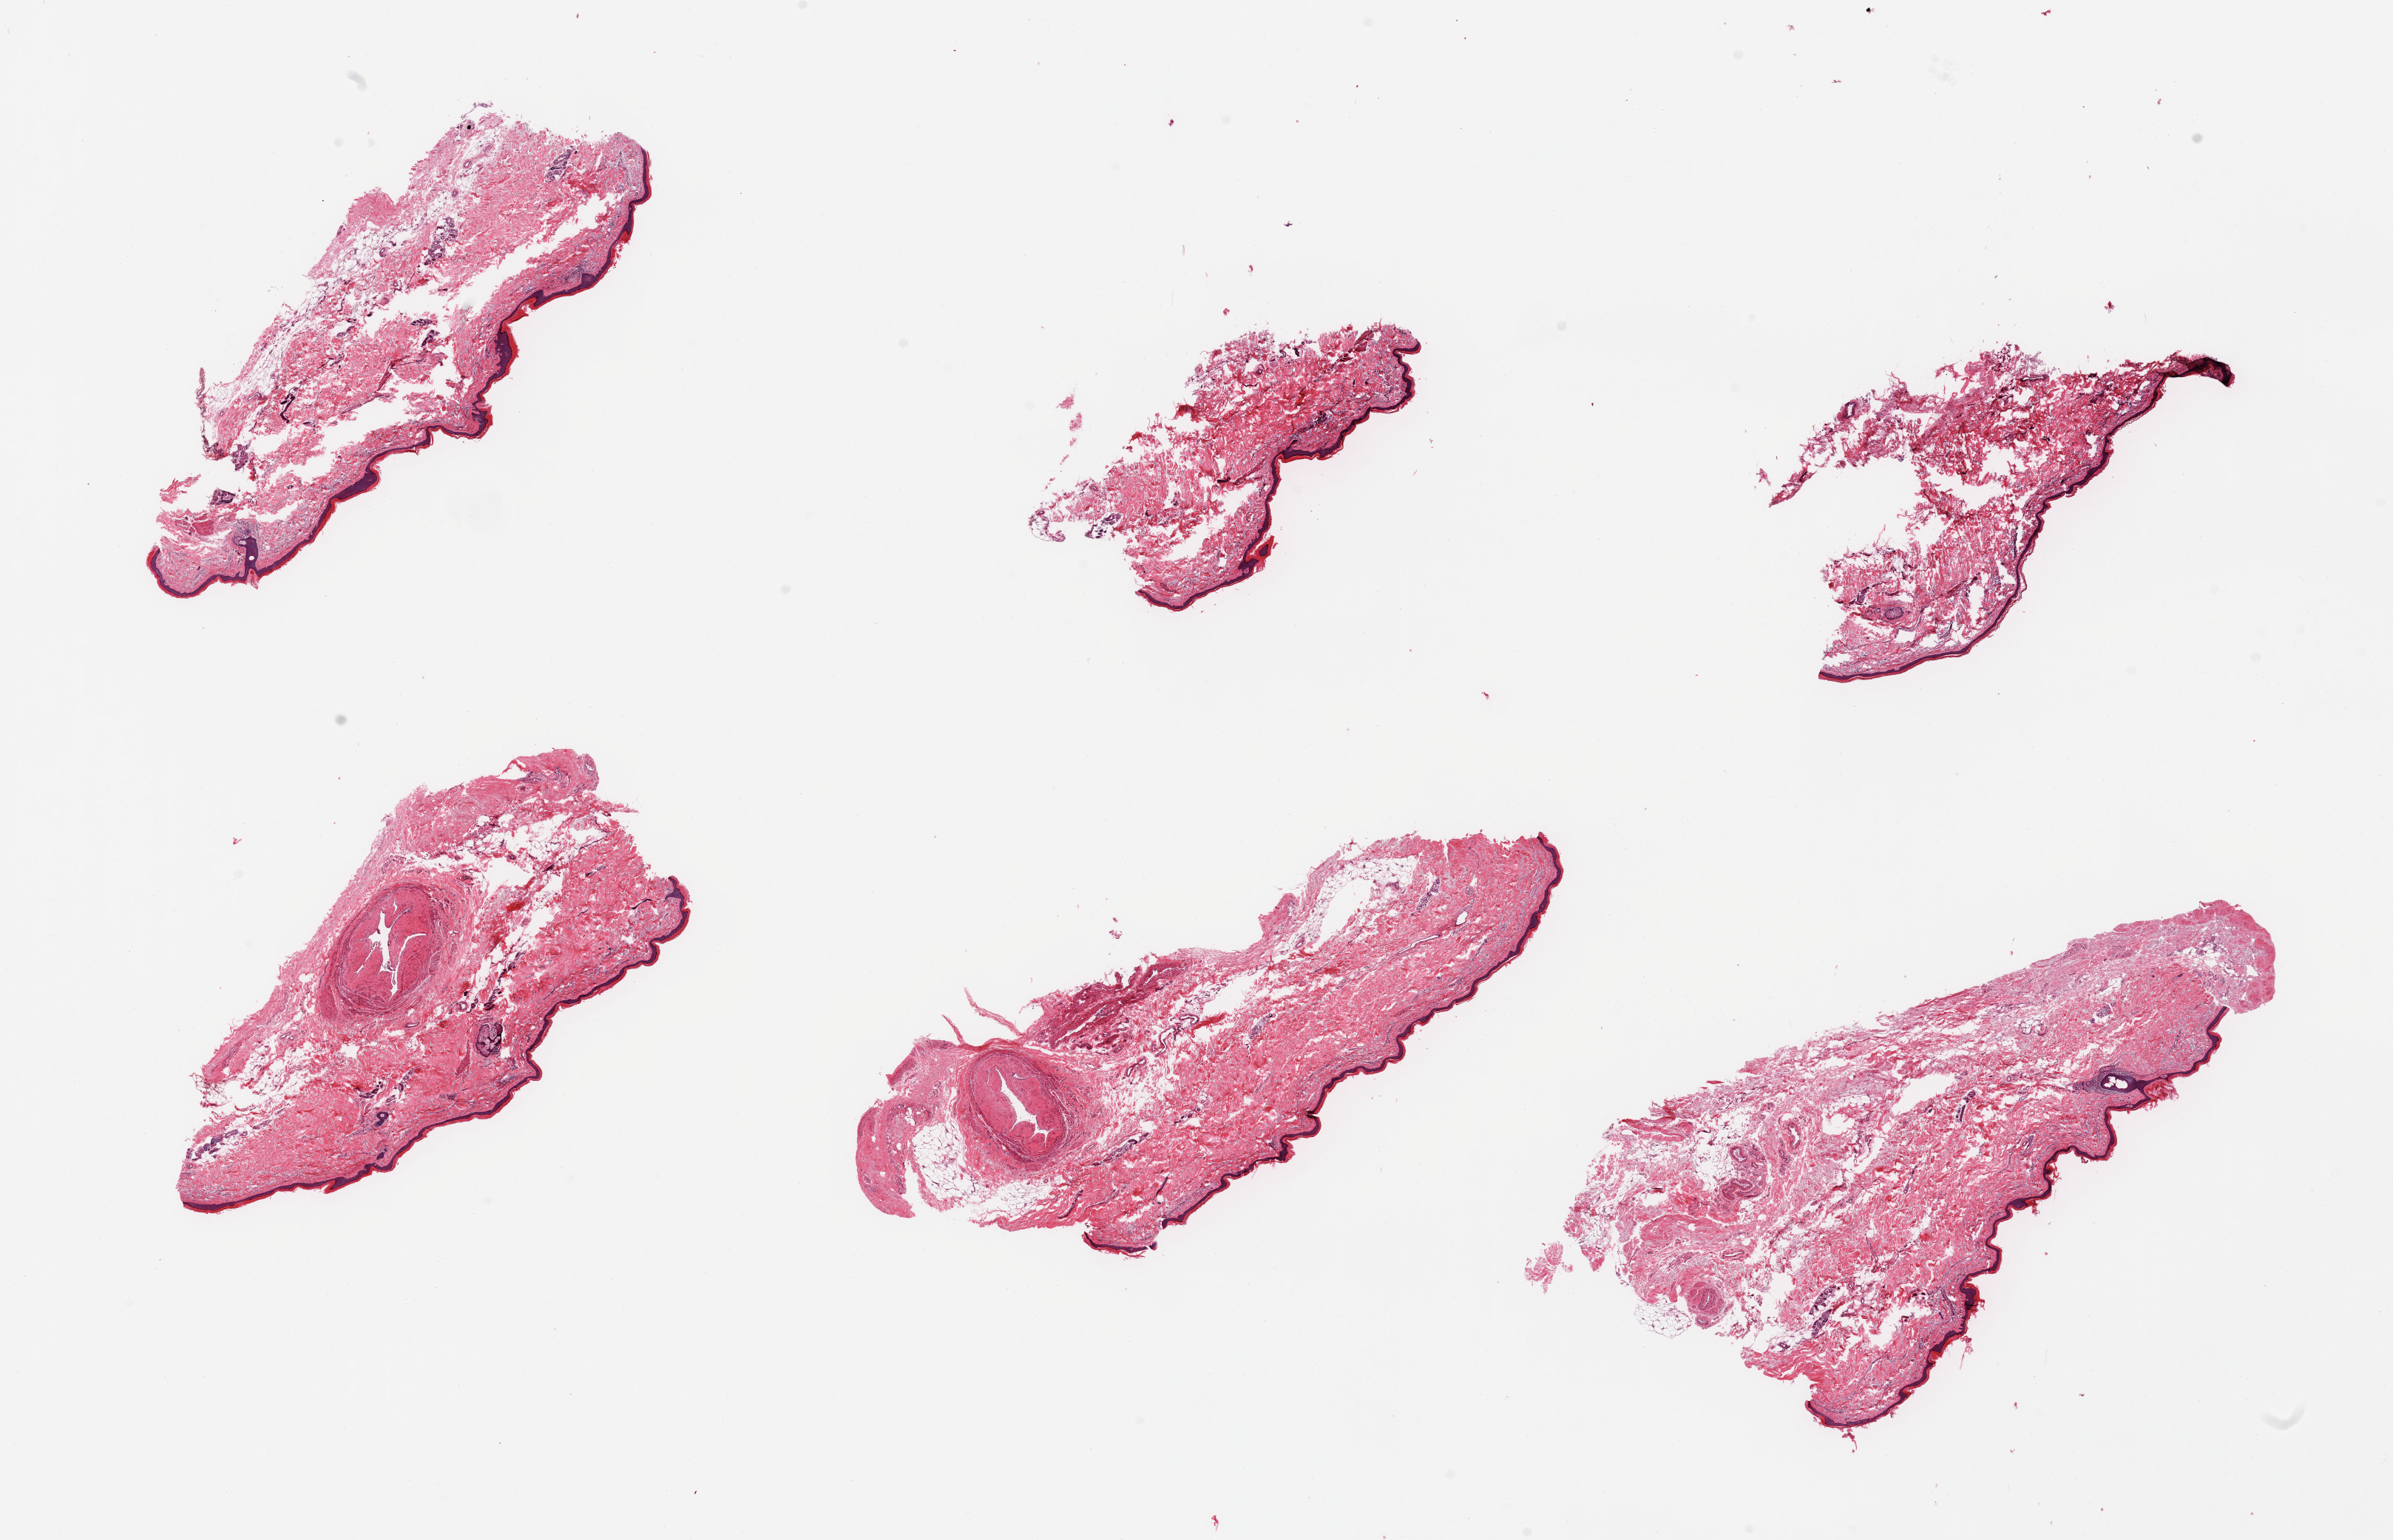
Digitized haematoxylin and eosin-stained section — low-resolution overview of the scanned area, about 25.6 x 16.5 mm (slide scanned at 20x). PAXgene-fixed, paraffin-embedded tissue. Target tissue: skin of lower leg. Donor tissue sample. Donor: male.
- reviewer comment on this tissue sample: 6 pieces, no dermal fat; squamous epithelium is ~50 microns